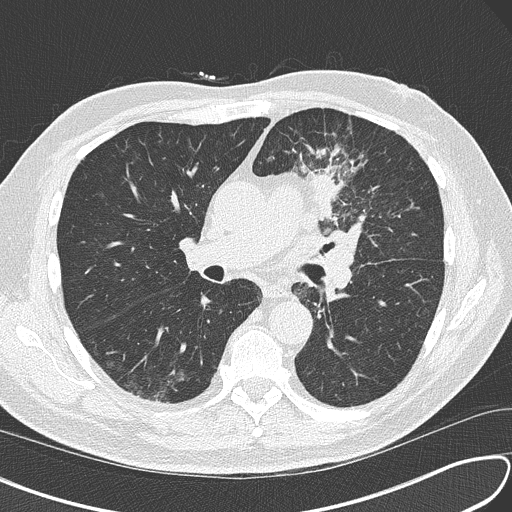
Low-dose screening chest CT, axial slice, third screening round (two years after baseline), lung window (W 1500 / L -600 HU), 120 kVp, 512 × 512 image matrix. Male participant, aged 67 years at enrolment. Current smoker at enrolment.
Expert-annotated lung lesion, bounding box <292,154,392,242> (left, top, right, bottom; pixels). Reader record for this screening exam (exam-level; its link to the box is not recorded): non-calcified nodule or mass ≥4 mm, left upper lobe, 30 × 23 mm, soft tissue attenuation, pre-existing on the prior screen: no. Official screen result: positive, other. Lung cancer was diagnosed 41 days after this screen: small cell carcinoma, NOS, left upper lobe, stage IV (AJCC 6th edition), 30 mm at pathology.